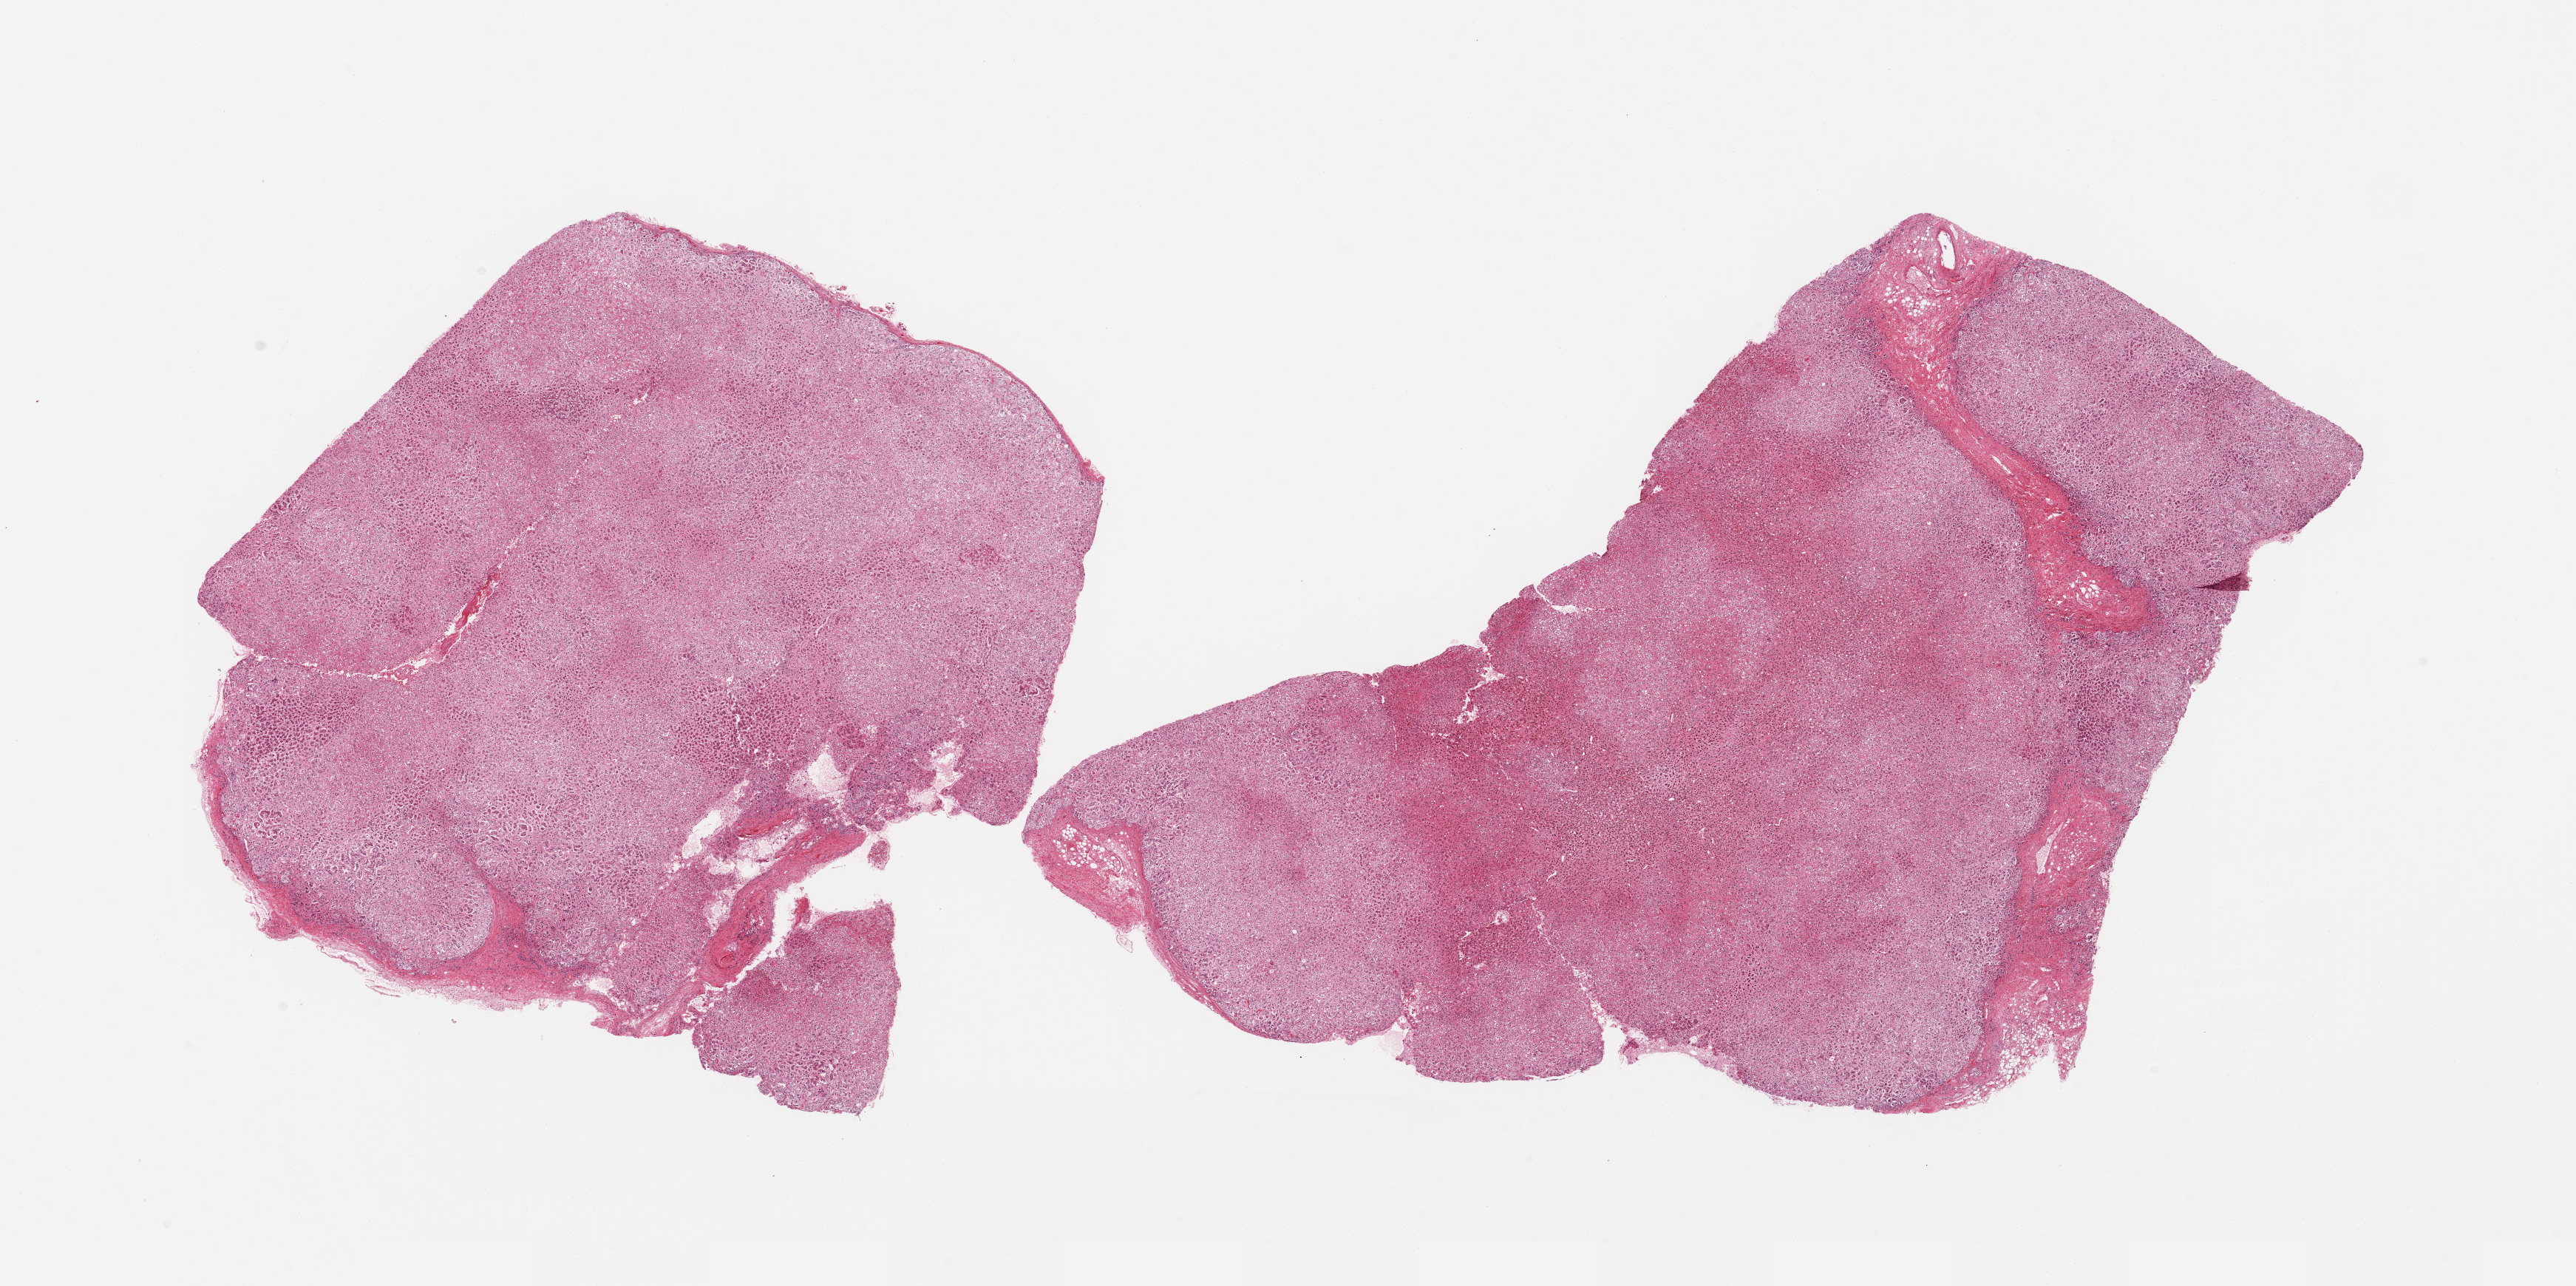
Digitized H&E-stained section, whole scanned area (about 27.6 x 13.8 mm) shown as a low-resolution overview, PAXgene-fixed, paraffin-embedded tissue, section of adrenal gland (target tissue), tissue donor sample. Male donor.
Review note (as recorded): 2 pieces, cortex, moderately advanced autolysis.